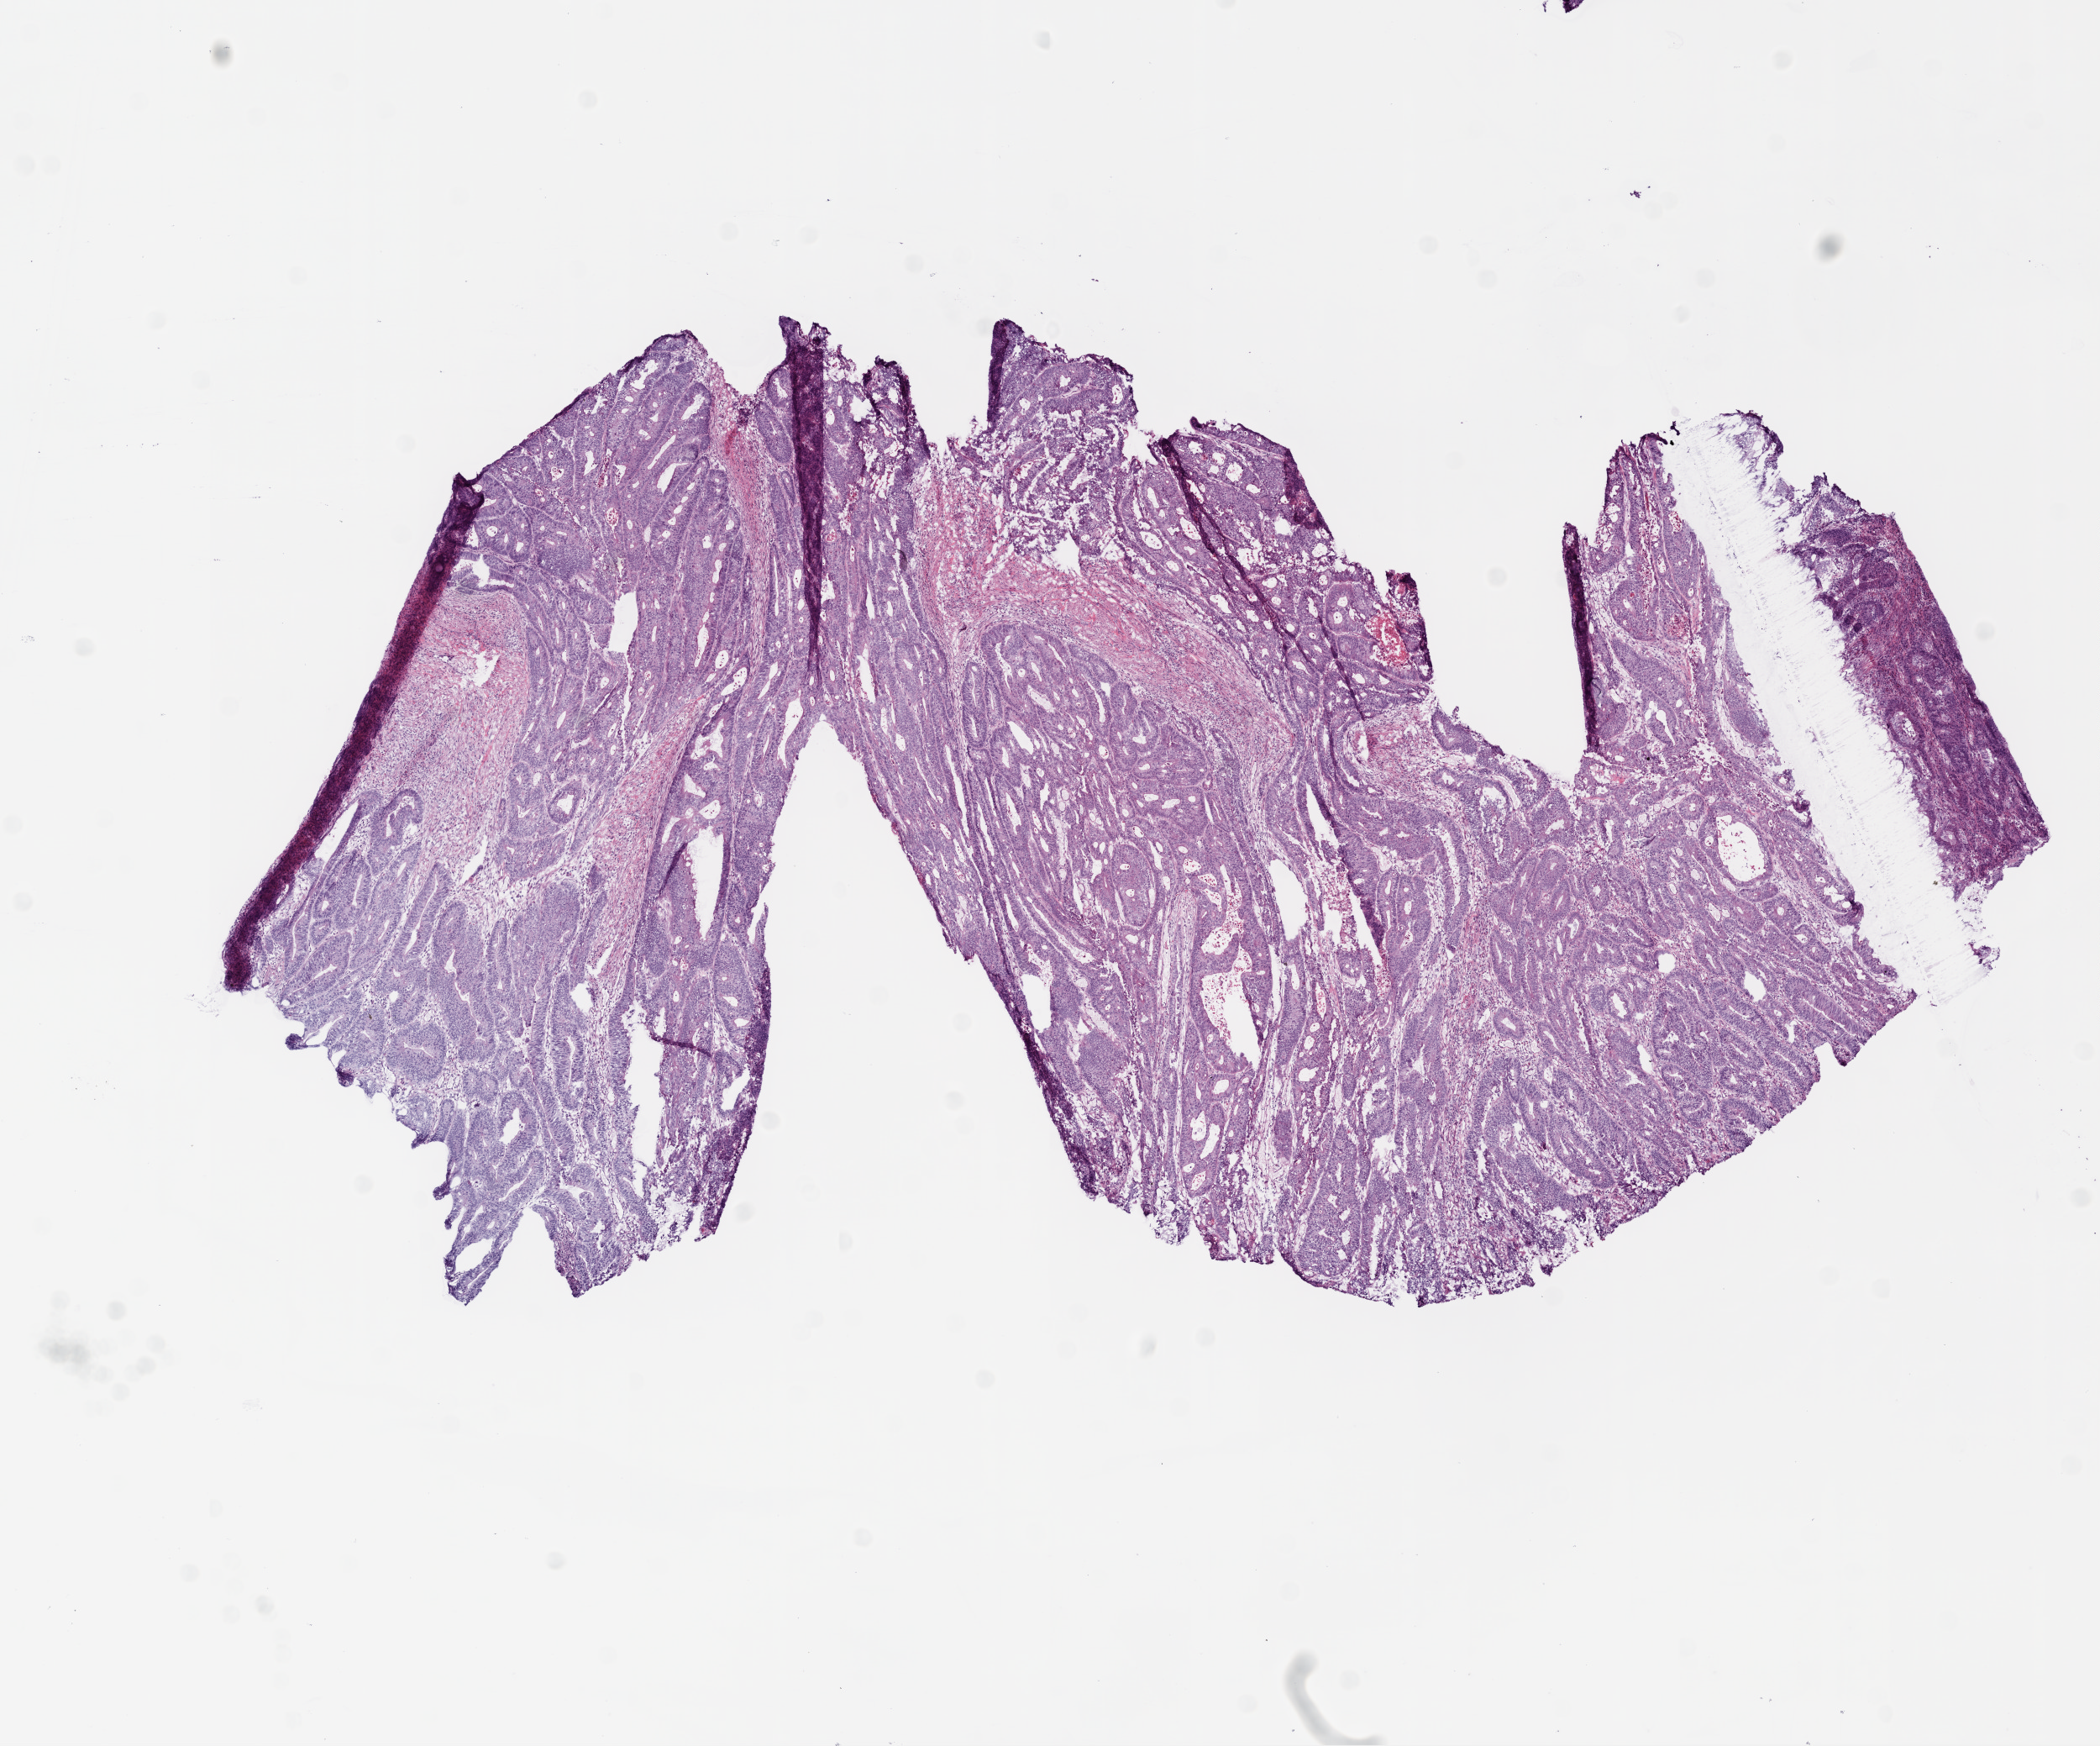
H&E-stained whole-slide image, a low-resolution overview of the entire scanned area, about 10.0 x 8.3 mm, frozen section from the top of the tissue portion, sample: primary tumour, rectum. Male, age 65 years at initial diagnosis. Pathologist review of this section (percent, as recorded): tumour cells 83%, tumour nuclei 80%, normal cells 0%, stromal cells 12%, necrosis 5%.
AJCC pathologic stage: IIA (6th edition). Lymph nodes positive (case pathology): 0 of 15 examined. Pathologic diagnosis: Adenocarcinoma, NOS.